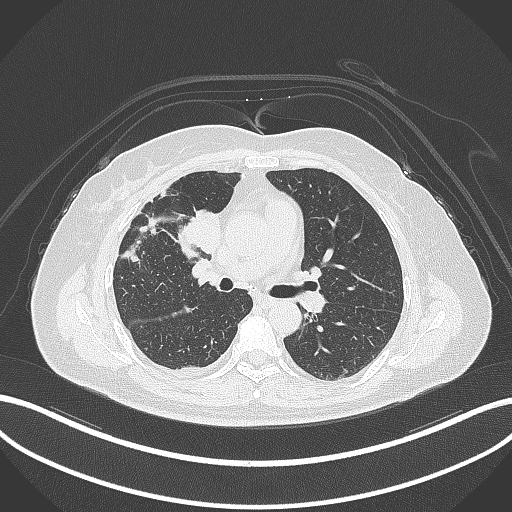
Chest CT, one axial slice; slice 160 of 305 in the series (ordered by position); lung window (W 1500 / L -600 HU); 1 mm slice thickness; 512 × 512 image matrix. Patient: female, 52 years. Case-level facts recorded for this patient, not image findings: clinical TNM (as recorded): T3 N1 M1.
Annotated regions visible in this slice (bounding box drawn by a radiologist):
- lung tumour (recorded histology: adenocarcinoma): bounding box <174,206,221,258> (left, top, right, bottom; pixels)